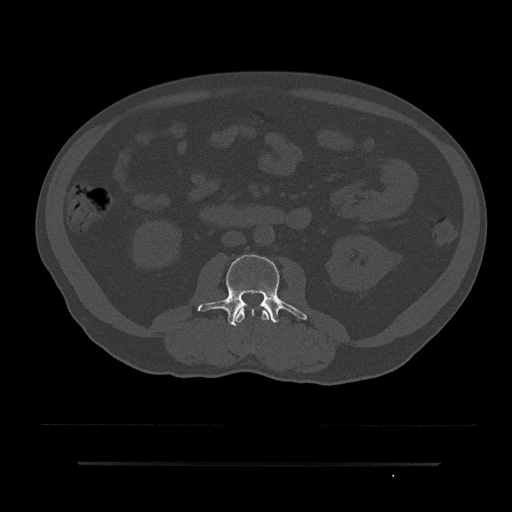
CT including the spine, one axial slice. Slice 20 of 797 in the series (ordered by position). 120 kVp. Bone window (W 1800 / L 400 HU). 0.5 mm slice thickness. 512 × 512 image matrix. Male patient, age 59 years. Case-level facts recorded for this patient, not image findings: primary cancer: bile ducts.
Annotated regions visible in this slice (semi-automatically segmented with operator editing):
- L2 vertebra: box from (x=234, y=306) to (x=271, y=323) px
- L3 vertebra: (x=197, y=254)–(x=307, y=326)